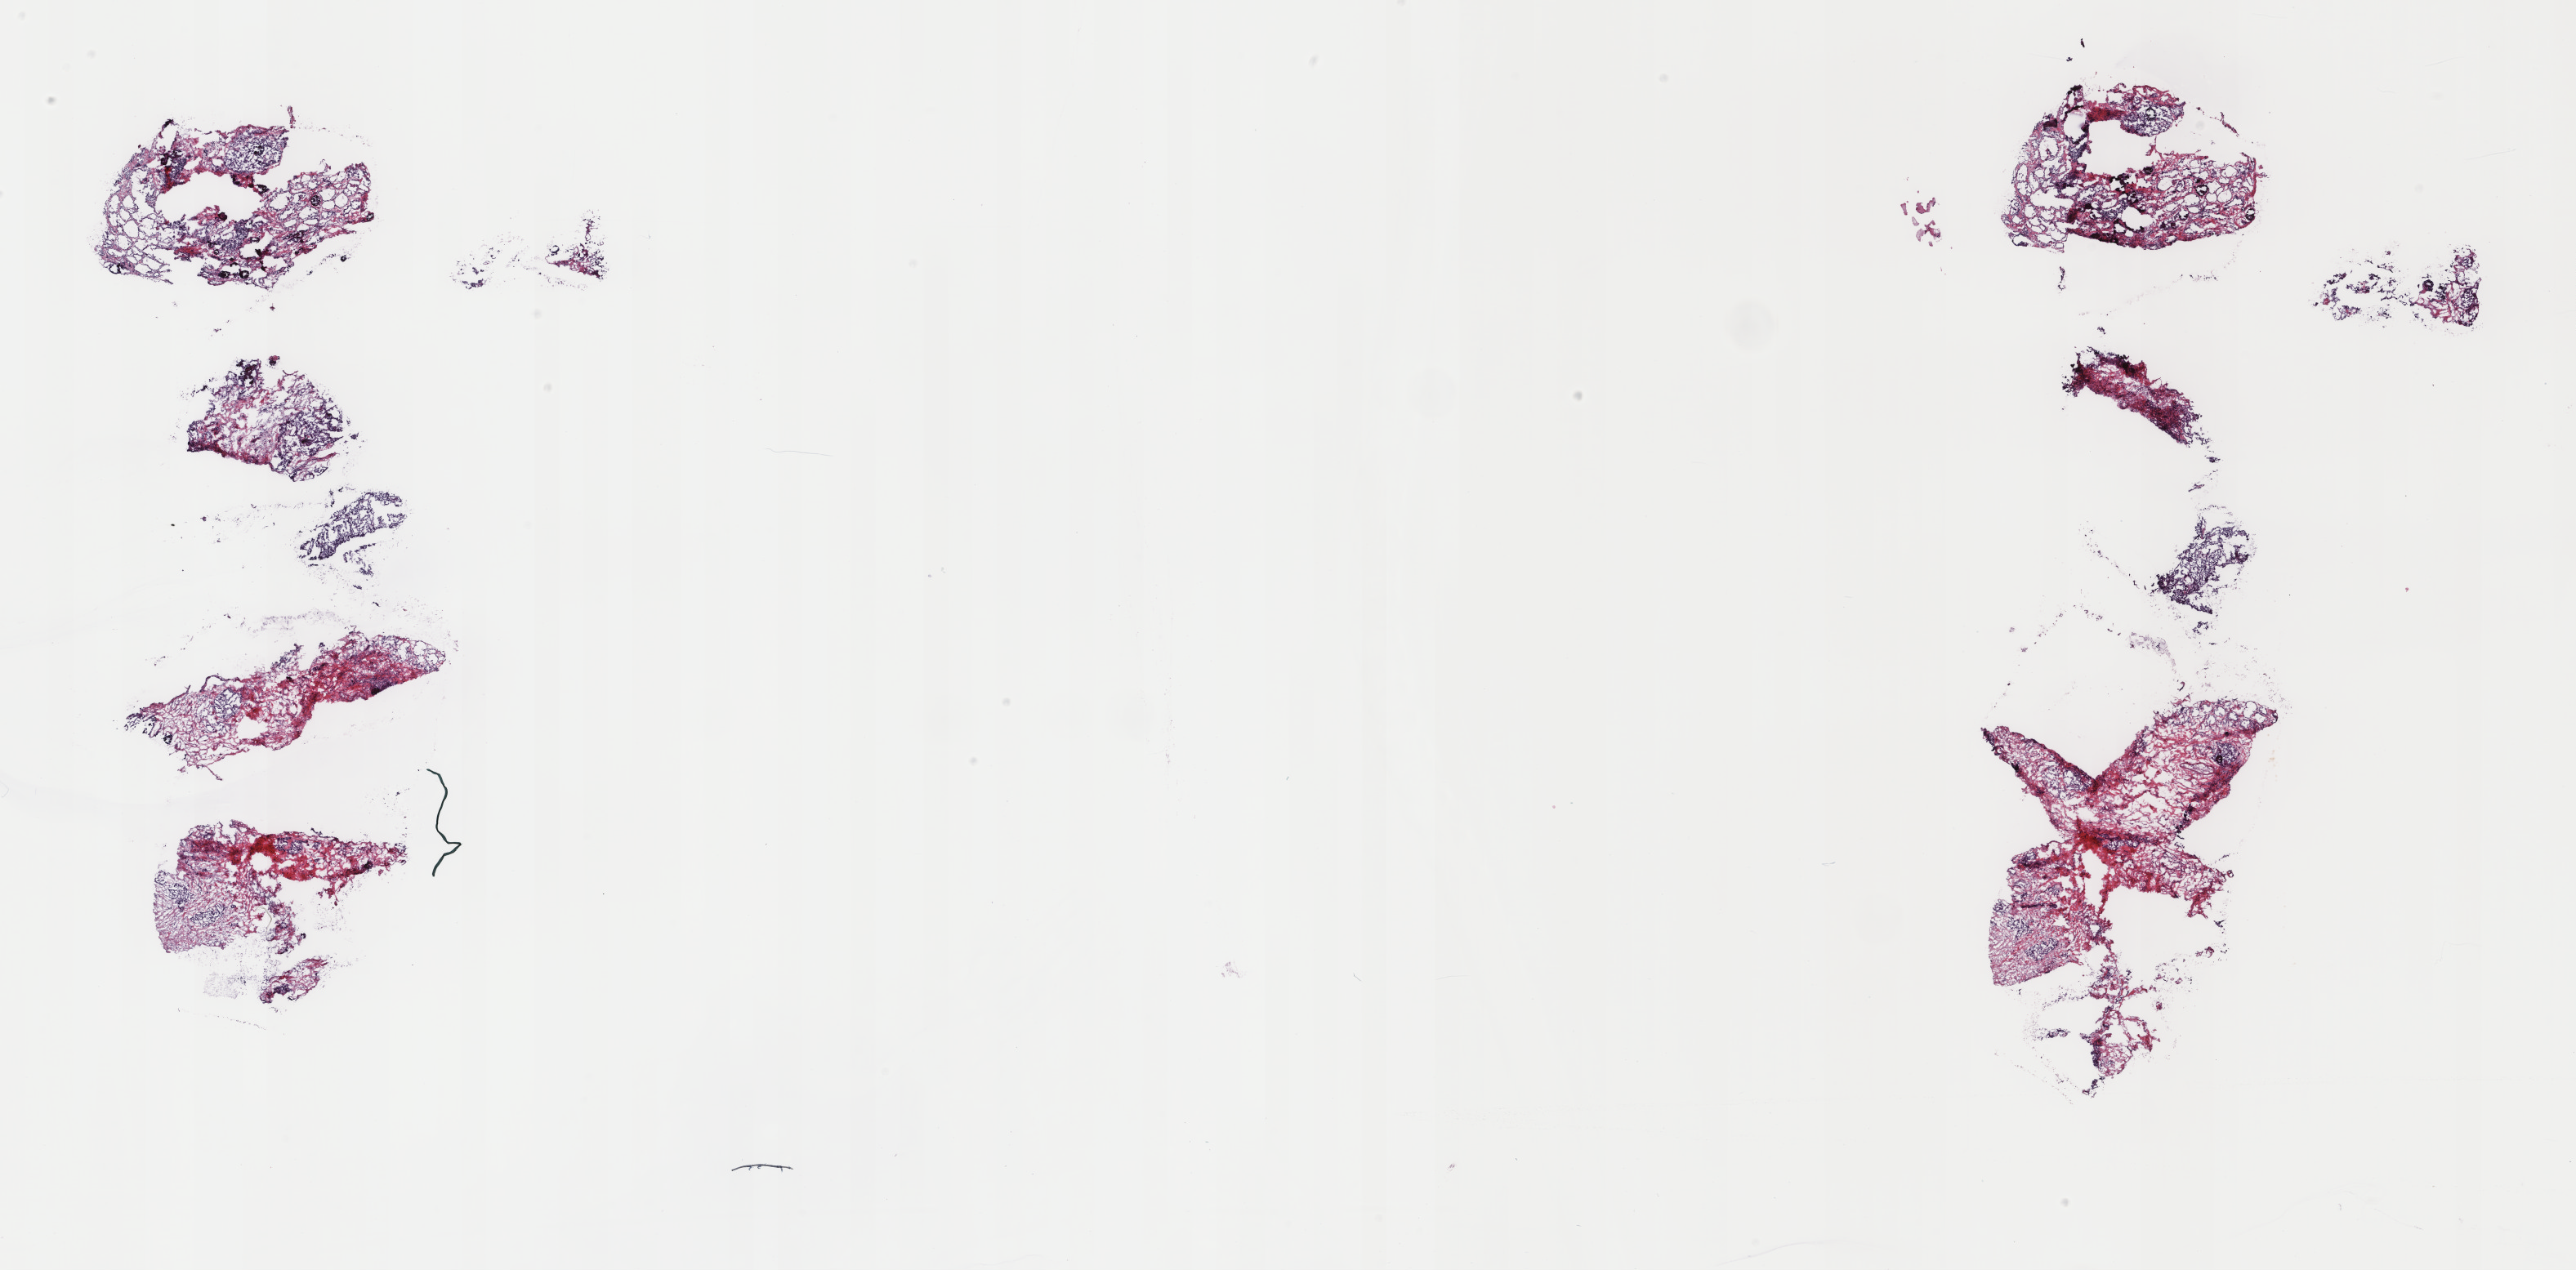
Whole-slide histology image, H&E, low-resolution overview of the scanned area, about 25.0 x 12.3 mm (from a 40x scan). Frozen section. Thyroid, primary tumour sample. Patient: female, age at initial diagnosis 19 years. Composition of this section per pathologist review: tumour cells 70%, tumour nuclei 70%, normal cells 3%, stromal cells 27%, necrosis 0%. Inflammatory infiltration, as recorded: lymphocyte infiltration 3%, monocyte infiltration 1%, neutrophil infiltration 0%.
Laterality: right. Histologic diagnosis: Papillary adenocarcinoma, NOS (thyroid gland). Lymph nodes positive (case pathology): 41 of 66 examined. AJCC pathologic stage: I (7th edition).